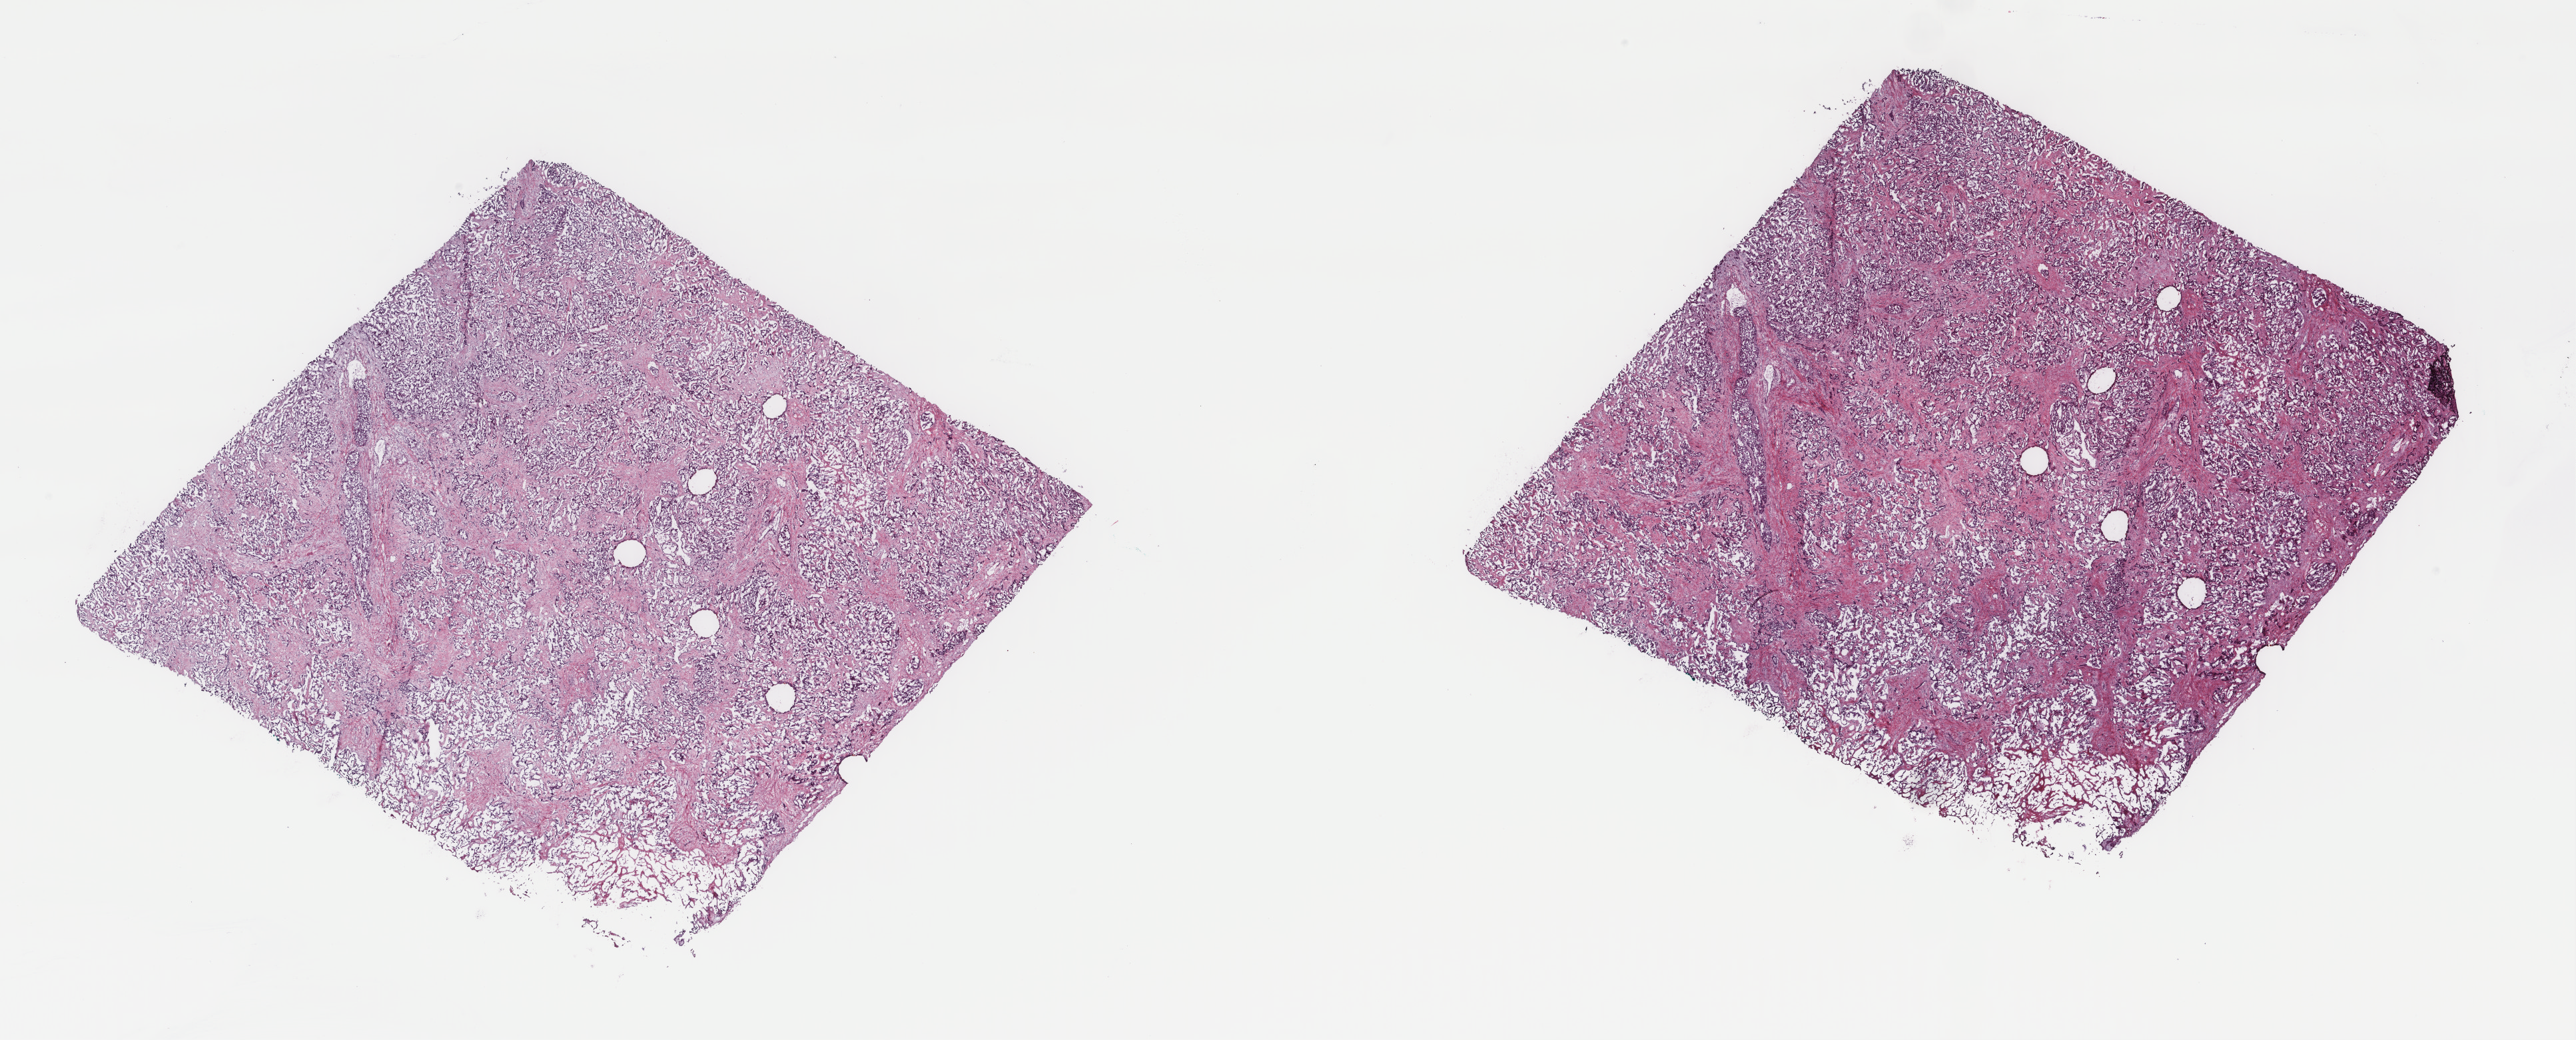
H&E whole-slide image — shown as a low-resolution overview of the whole scanned area (about 30.7 x 12.4 mm, slide scanned at 40x); frozen section from the top of the tissue portion; sample: primary tumour, liver. Female, age 76 years at initial diagnosis. Histologic grade: G2 (moderately differentiated). Pathologist review of this section (percent, as recorded): tumour cells 100%, tumour nuclei 85%, normal cells 0%, stromal cells 0%, necrosis 0%. Infiltration values recorded for this section: lymphocyte infiltration 1%, monocyte infiltration 0%, neutrophil infiltration 0%.
AJCC pathologic stage: II (7th edition). Histologic diagnosis: Hepatocellular carcinoma, fibrolamellar.